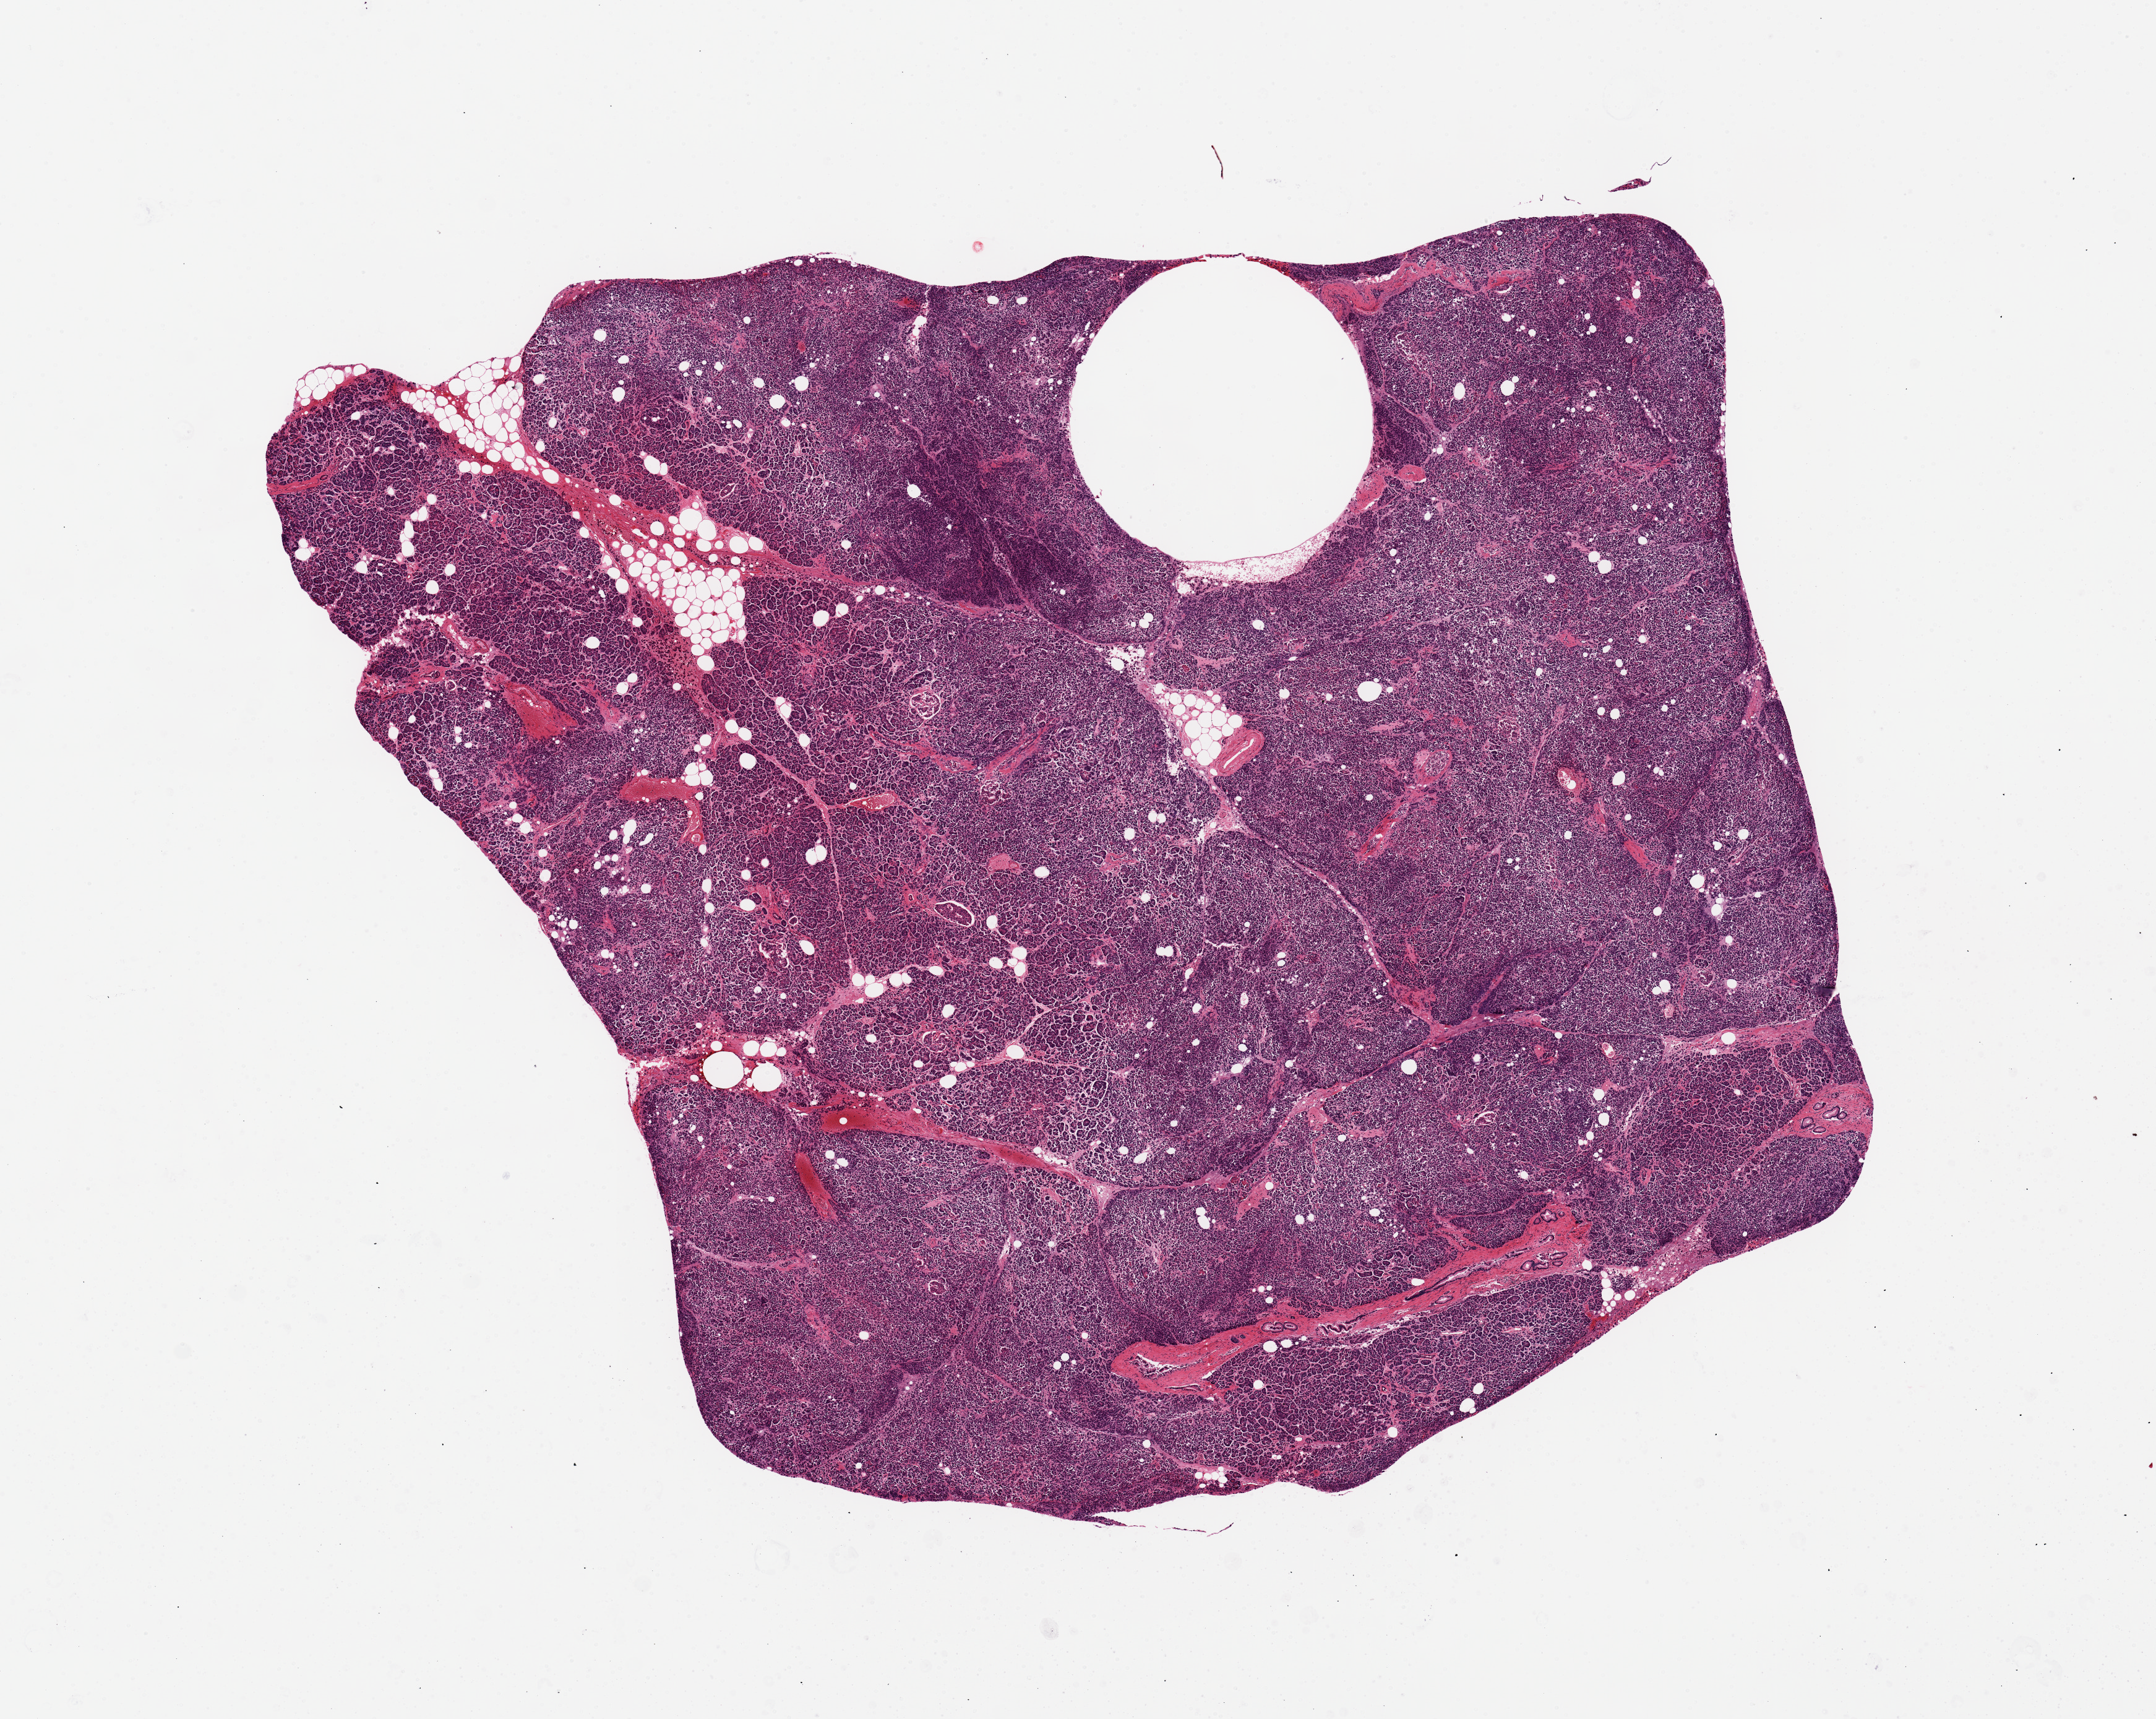
Hematoxylin and eosin (H&E) whole-slide image, brightfield — a low-resolution overview of the entire scanned area, about 13.8 x 11.0 mm (from a 20x scan). PAXgene-fixed, paraffin-embedded tissue. Section of pancreas (target tissue). Tissue donor sample. Donor: female.
Review note (as recorded): Mild-moderate autolysis.